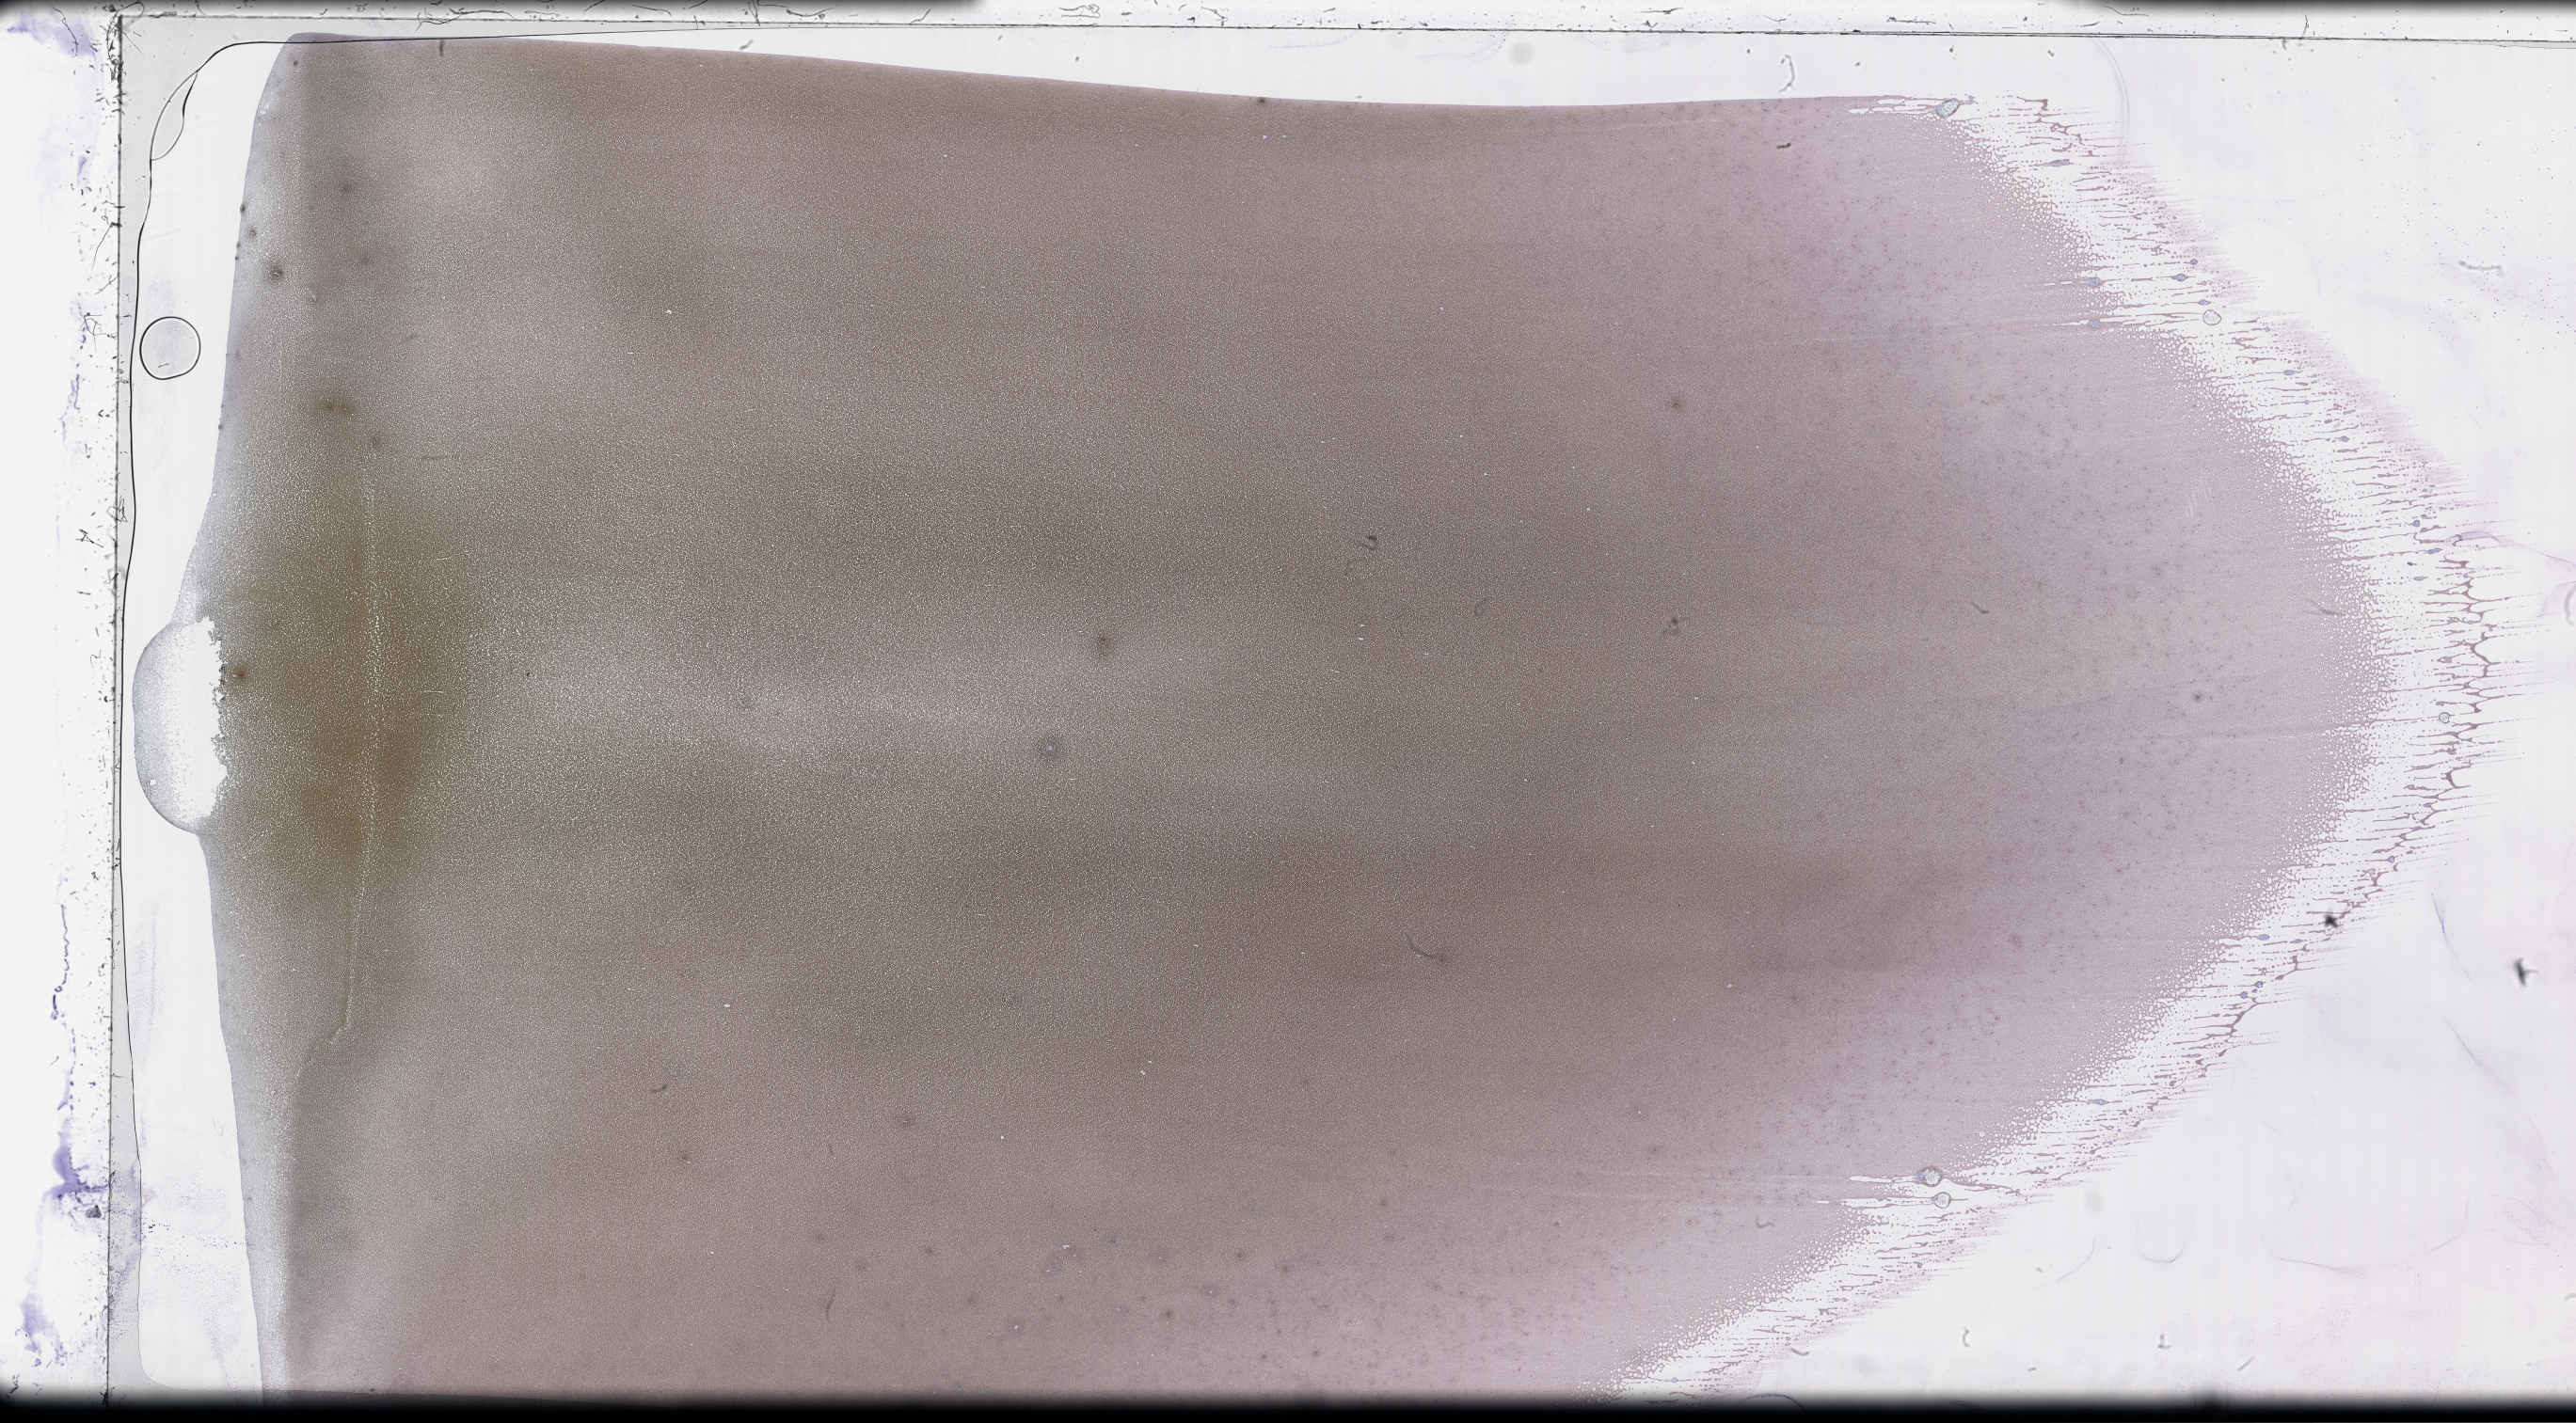
Wright-Giemsa-stained whole blood smear, whole-slide image — low-resolution overview of the scanned area, about 44.2 x 24.4 mm. EDTA-anticoagulated smear. Male patient.
* from a patient with: Plasma Cell Myeloma